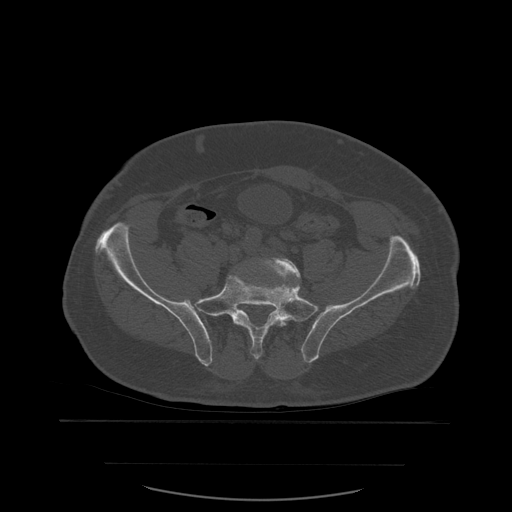
CT including the spine, one axial slice; position 120 of 590 along the scan axis; bone window (W 1800 / L 400 HU); 1.25 mm slice thickness; 512 × 512 image matrix, field of view 479 × 479 mm. Patient age 71 years. From the clinical record (not read from this slice): primary cancer: lung.
Annotated regions visible in this slice (semi-automatically segmented with operator editing):
- L5 vertebra: bounding box <252,257,301,357> (left, top, right, bottom; pixels)